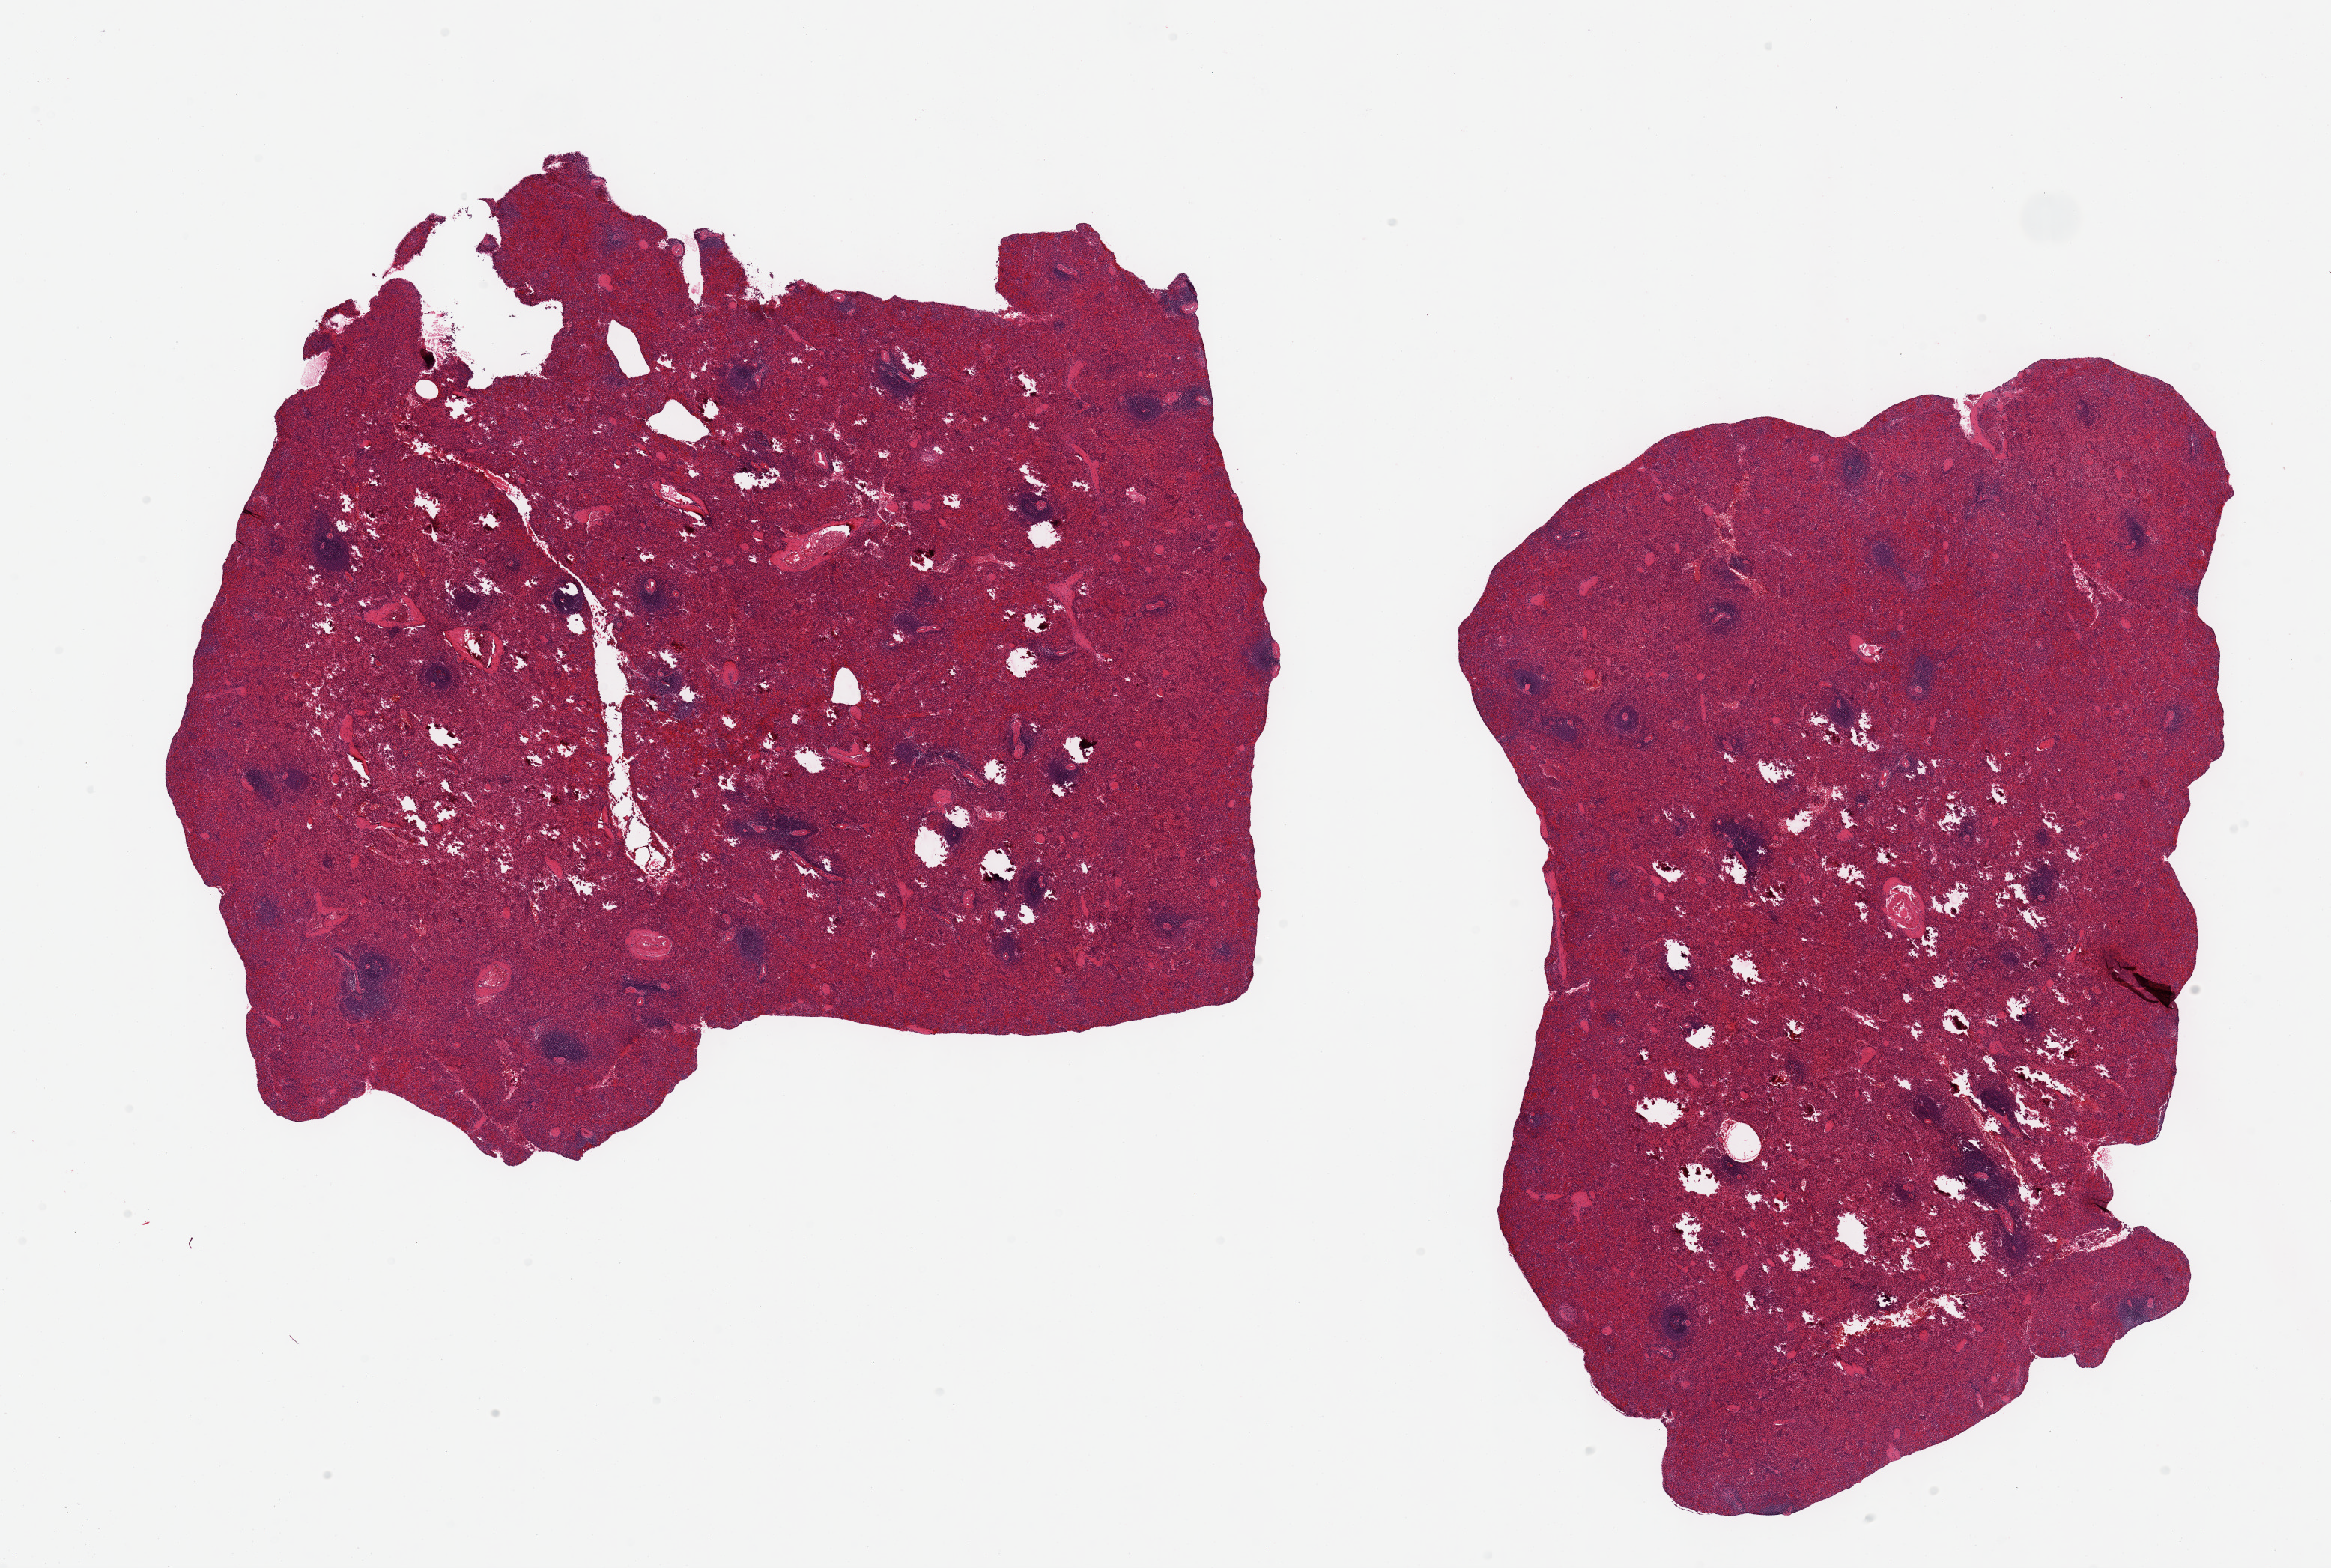
Whole-slide image, haematoxylin and eosin stain — low-resolution overview of the scanned area, about 24.6 x 16.6 mm (slide scanned at 20x). PAXgene-fixed paraffin-embedded (PFPE) section. Sampled site (target tissue): spleen. Donor tissue sample. Donor: male.
• review note (as recorded): 2 pieces, no abnormalities